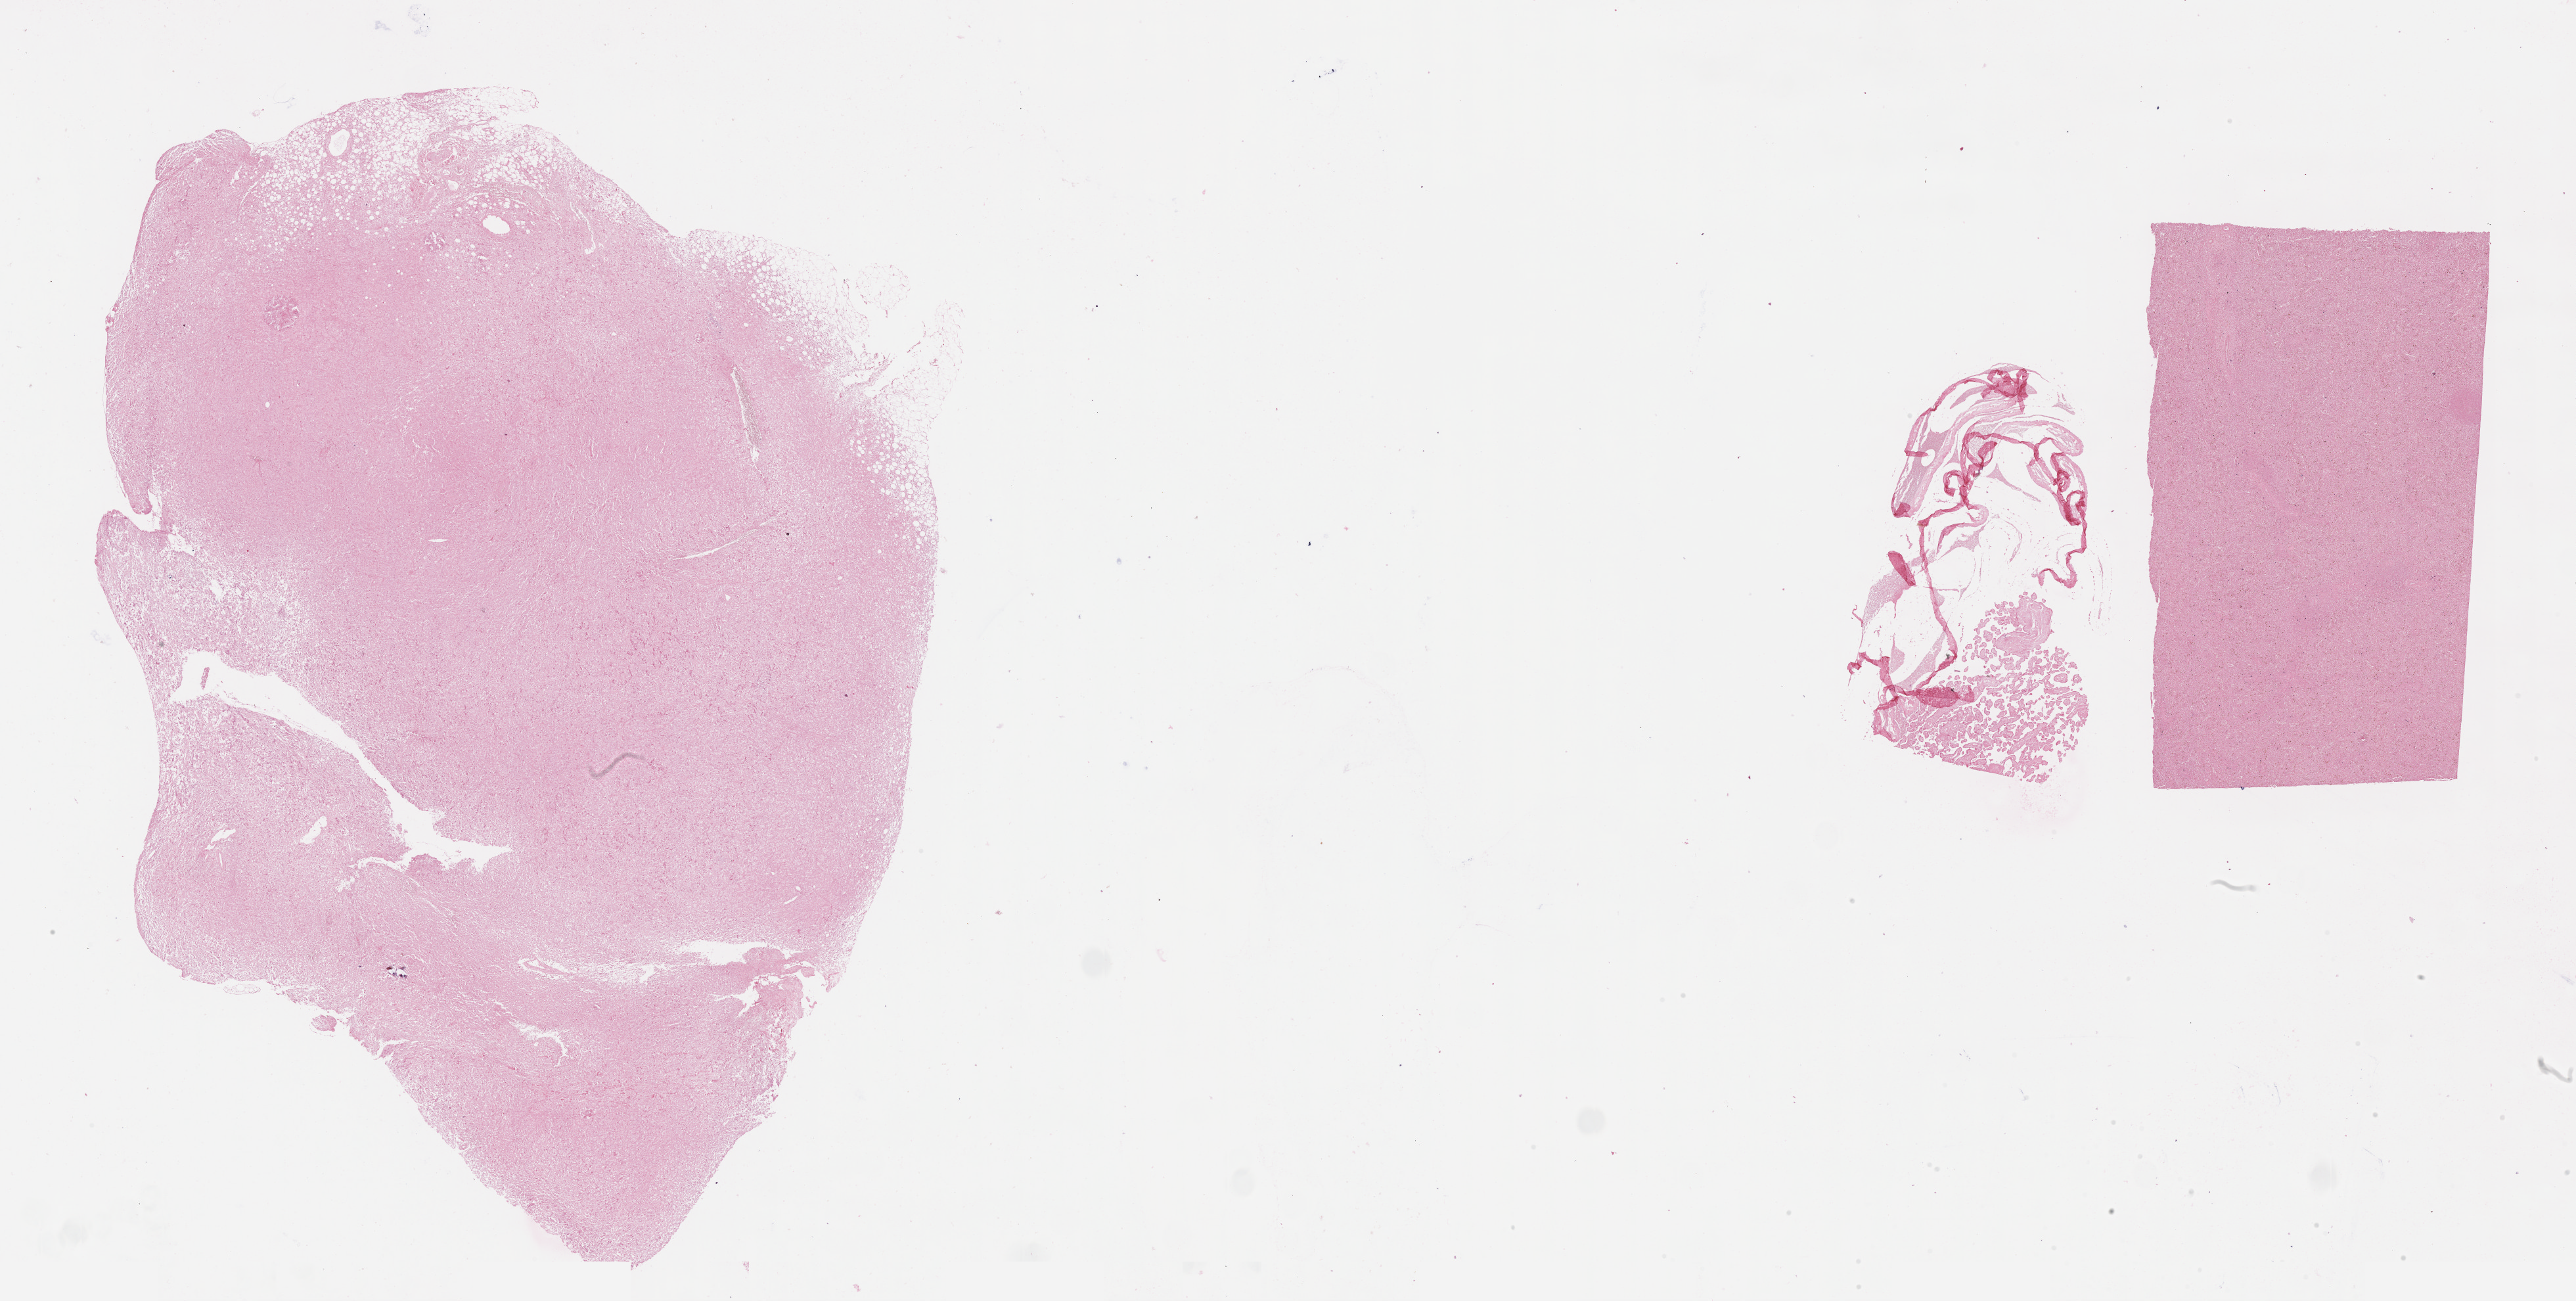
Whole-slide image, Epstein–Barr virus-encoded RNA (EBER) in-situ hybridisation — shown as a low-resolution overview of the whole scanned area (about 31.7 x 16.0 mm). Female patient.
- specimen: tumor tissue